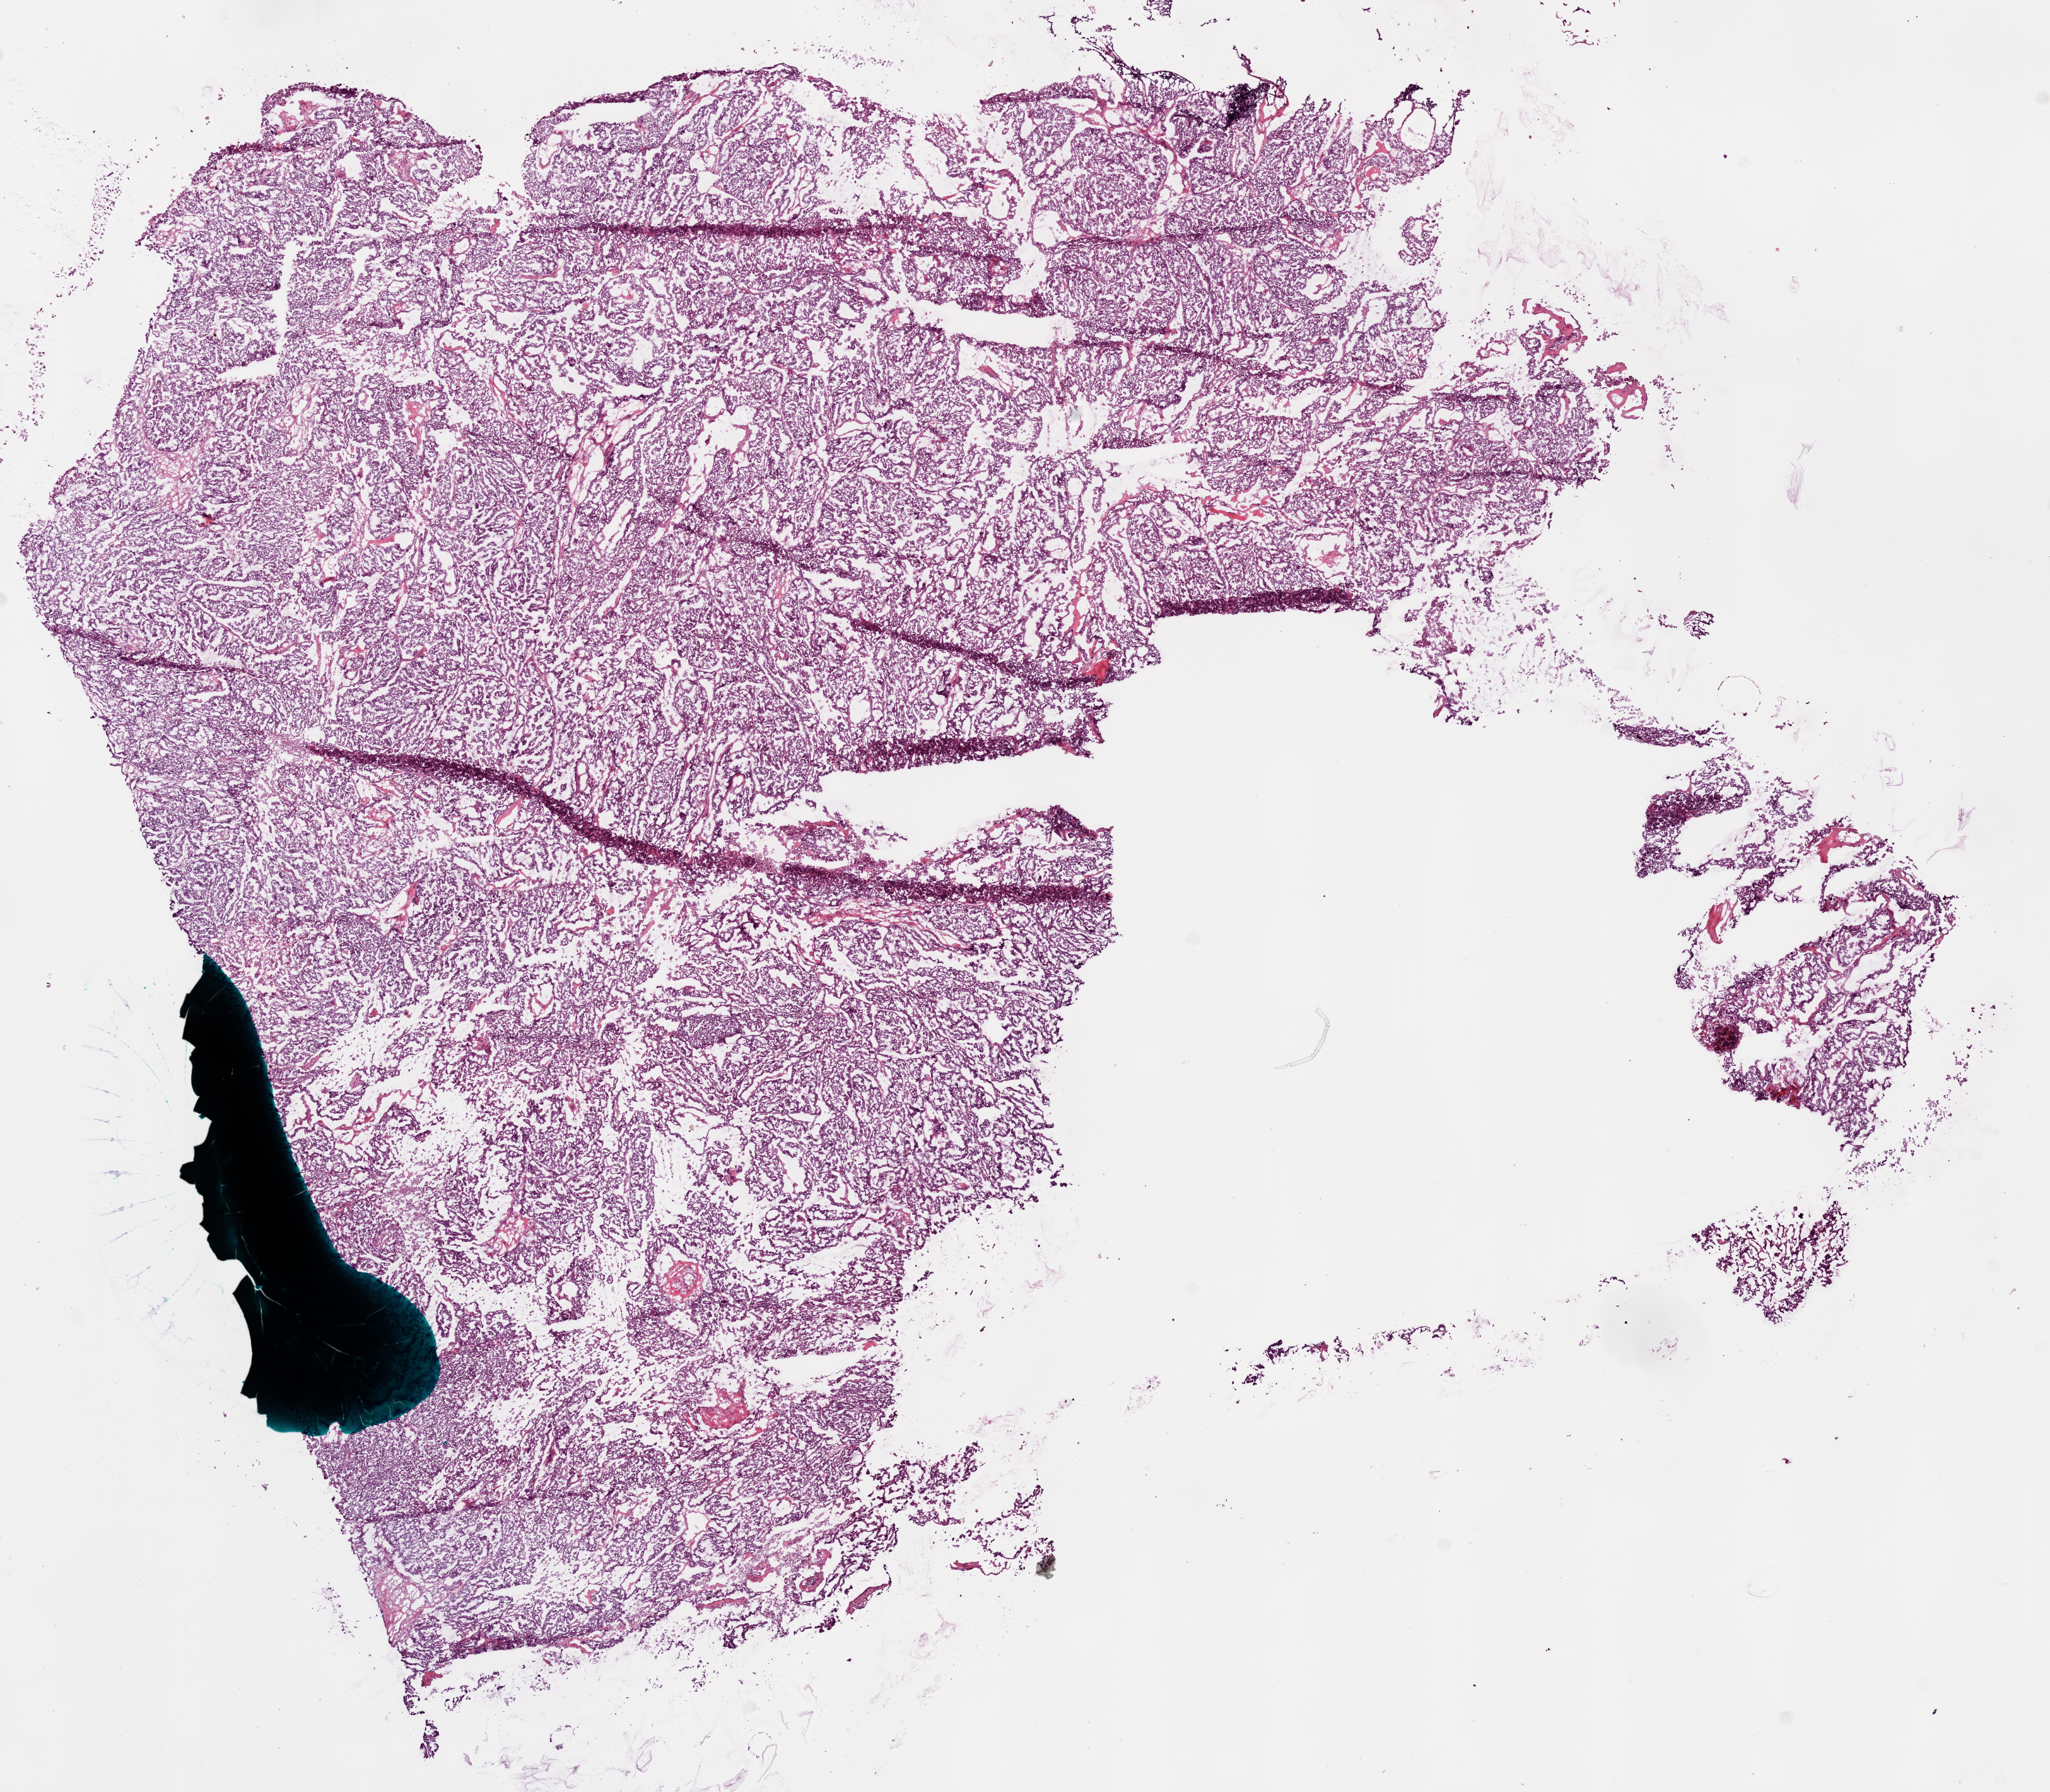
Digitized Hematoxylin and eosin (H&E) stained tissue section (whole slide) — whole scanned area (about 13.0 x 11.4 mm) shown as a low-resolution overview; frozen section from the bottom of the tissue portion; sample: primary tumour, ovary. Female patient; age at initial diagnosis 51 years. Histologic grade: G3 (poorly differentiated). Pathologist review of this section (percent, as recorded): tumour cells 94%, tumour nuclei 95%, normal cells 0%, stromal cells 5%, necrosis 1%.
- histologic diagnosis: Serous cystadenocarcinoma, NOS
- FIGO stage: IIIC